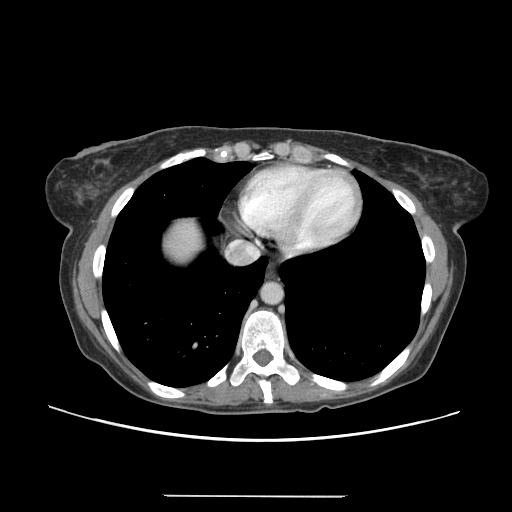
Contrast-enhanced abdominal CT, one axial slice; position 135 of 144 along the scan axis; intravenous contrast given; soft-tissue window (W 400 / L 40 HU); 2.5 mm slice thickness; 512 × 512 image matrix, field of view 380 × 380 mm. Female patient, age 53 years. From the clinical record (not read from this slice): diagnosis: colorectal cancer liver metastases, imaged before liver resection; multiple liver metastases: yes; largest metastasis: 1.1 cm; disease in both lobes: no.
Annotated regions visible in this slice (manually delineated by an expert):
- liver: bounding box [x1, y1, x2, y2] px = [164, 218, 203, 265]
- planned liver remnant (the part of the liver to remain after resection): [160, 218, 206, 268]